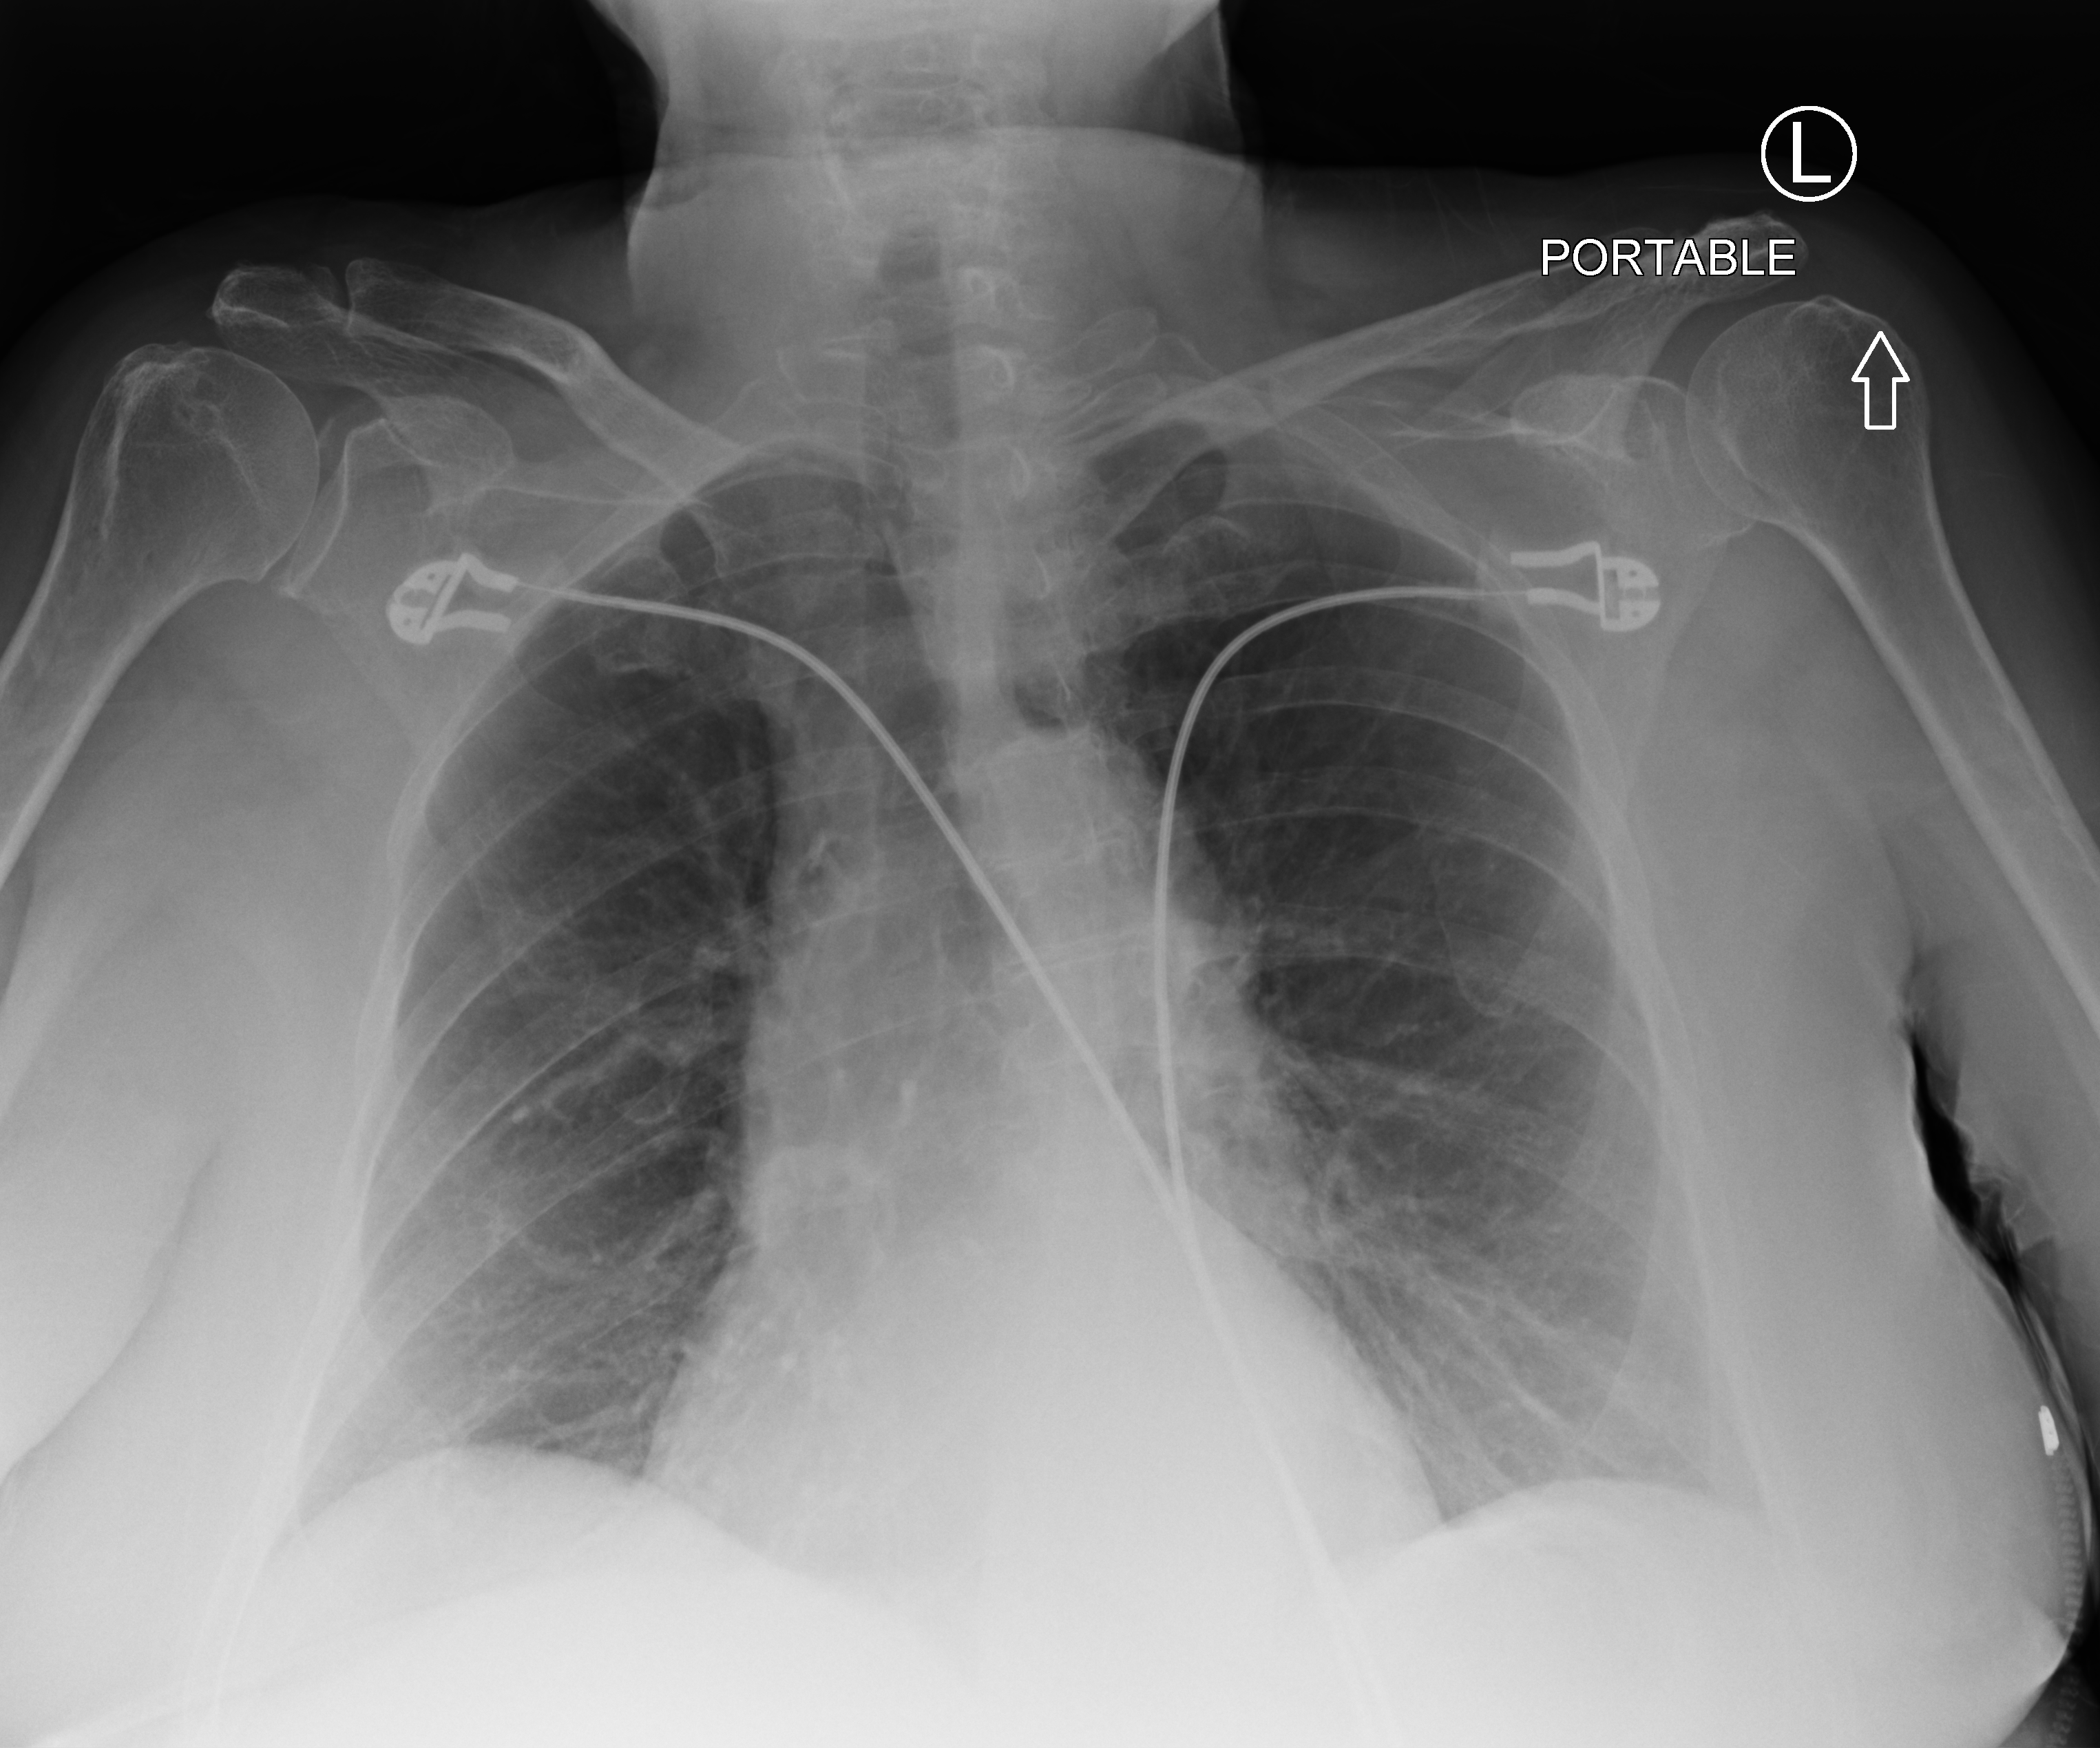
Bedside chest radiograph (computed radiography); anteroposterior (AP) projection. Female patient hospitalised with COVID-19, age 75–90 years.
From the hospital-stay record, not from the radiograph (when in the stay this image was taken is not recorded): COPD (admission record): no.